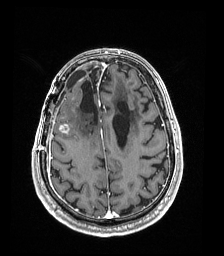
Brain MRI from a brain-tumour surgery series, one axial slice. Slice 56 of 192 in the series (ordered by position). T1-weighted post-contrast. 1 mm slice thickness. 224 × 256 image matrix, field of view 224 × 256 mm. Case-level facts recorded for this patient, not image findings: histopathology: Astrocytoma; WHO grade: 4; IDH mutation: yes.
Outlined on this slice (manually delineated by an expert):
- previous resection cavity: box from (x=80, y=69) to (x=98, y=123) px